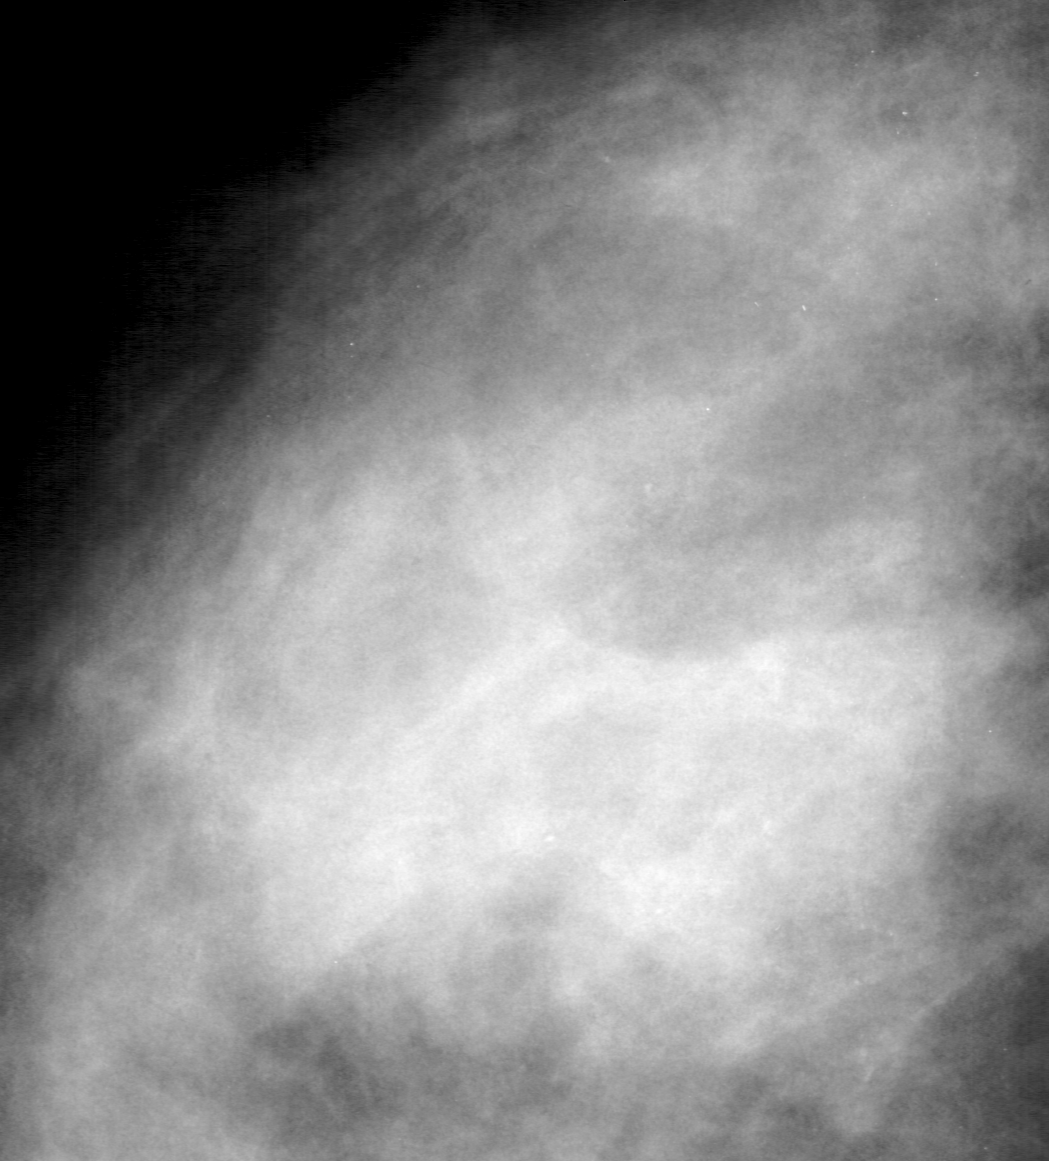
Region of interest cut from a scanned film mammogram (one marked finding); left breast; CC view.
Marked abnormality: calcifications, morphology pleomorphic, distribution segmental; BI-RADS assessment category 4; subtlety rating 1 on a 1 (subtle) to 5 (obvious) scale; pathology (as recorded): malignant.